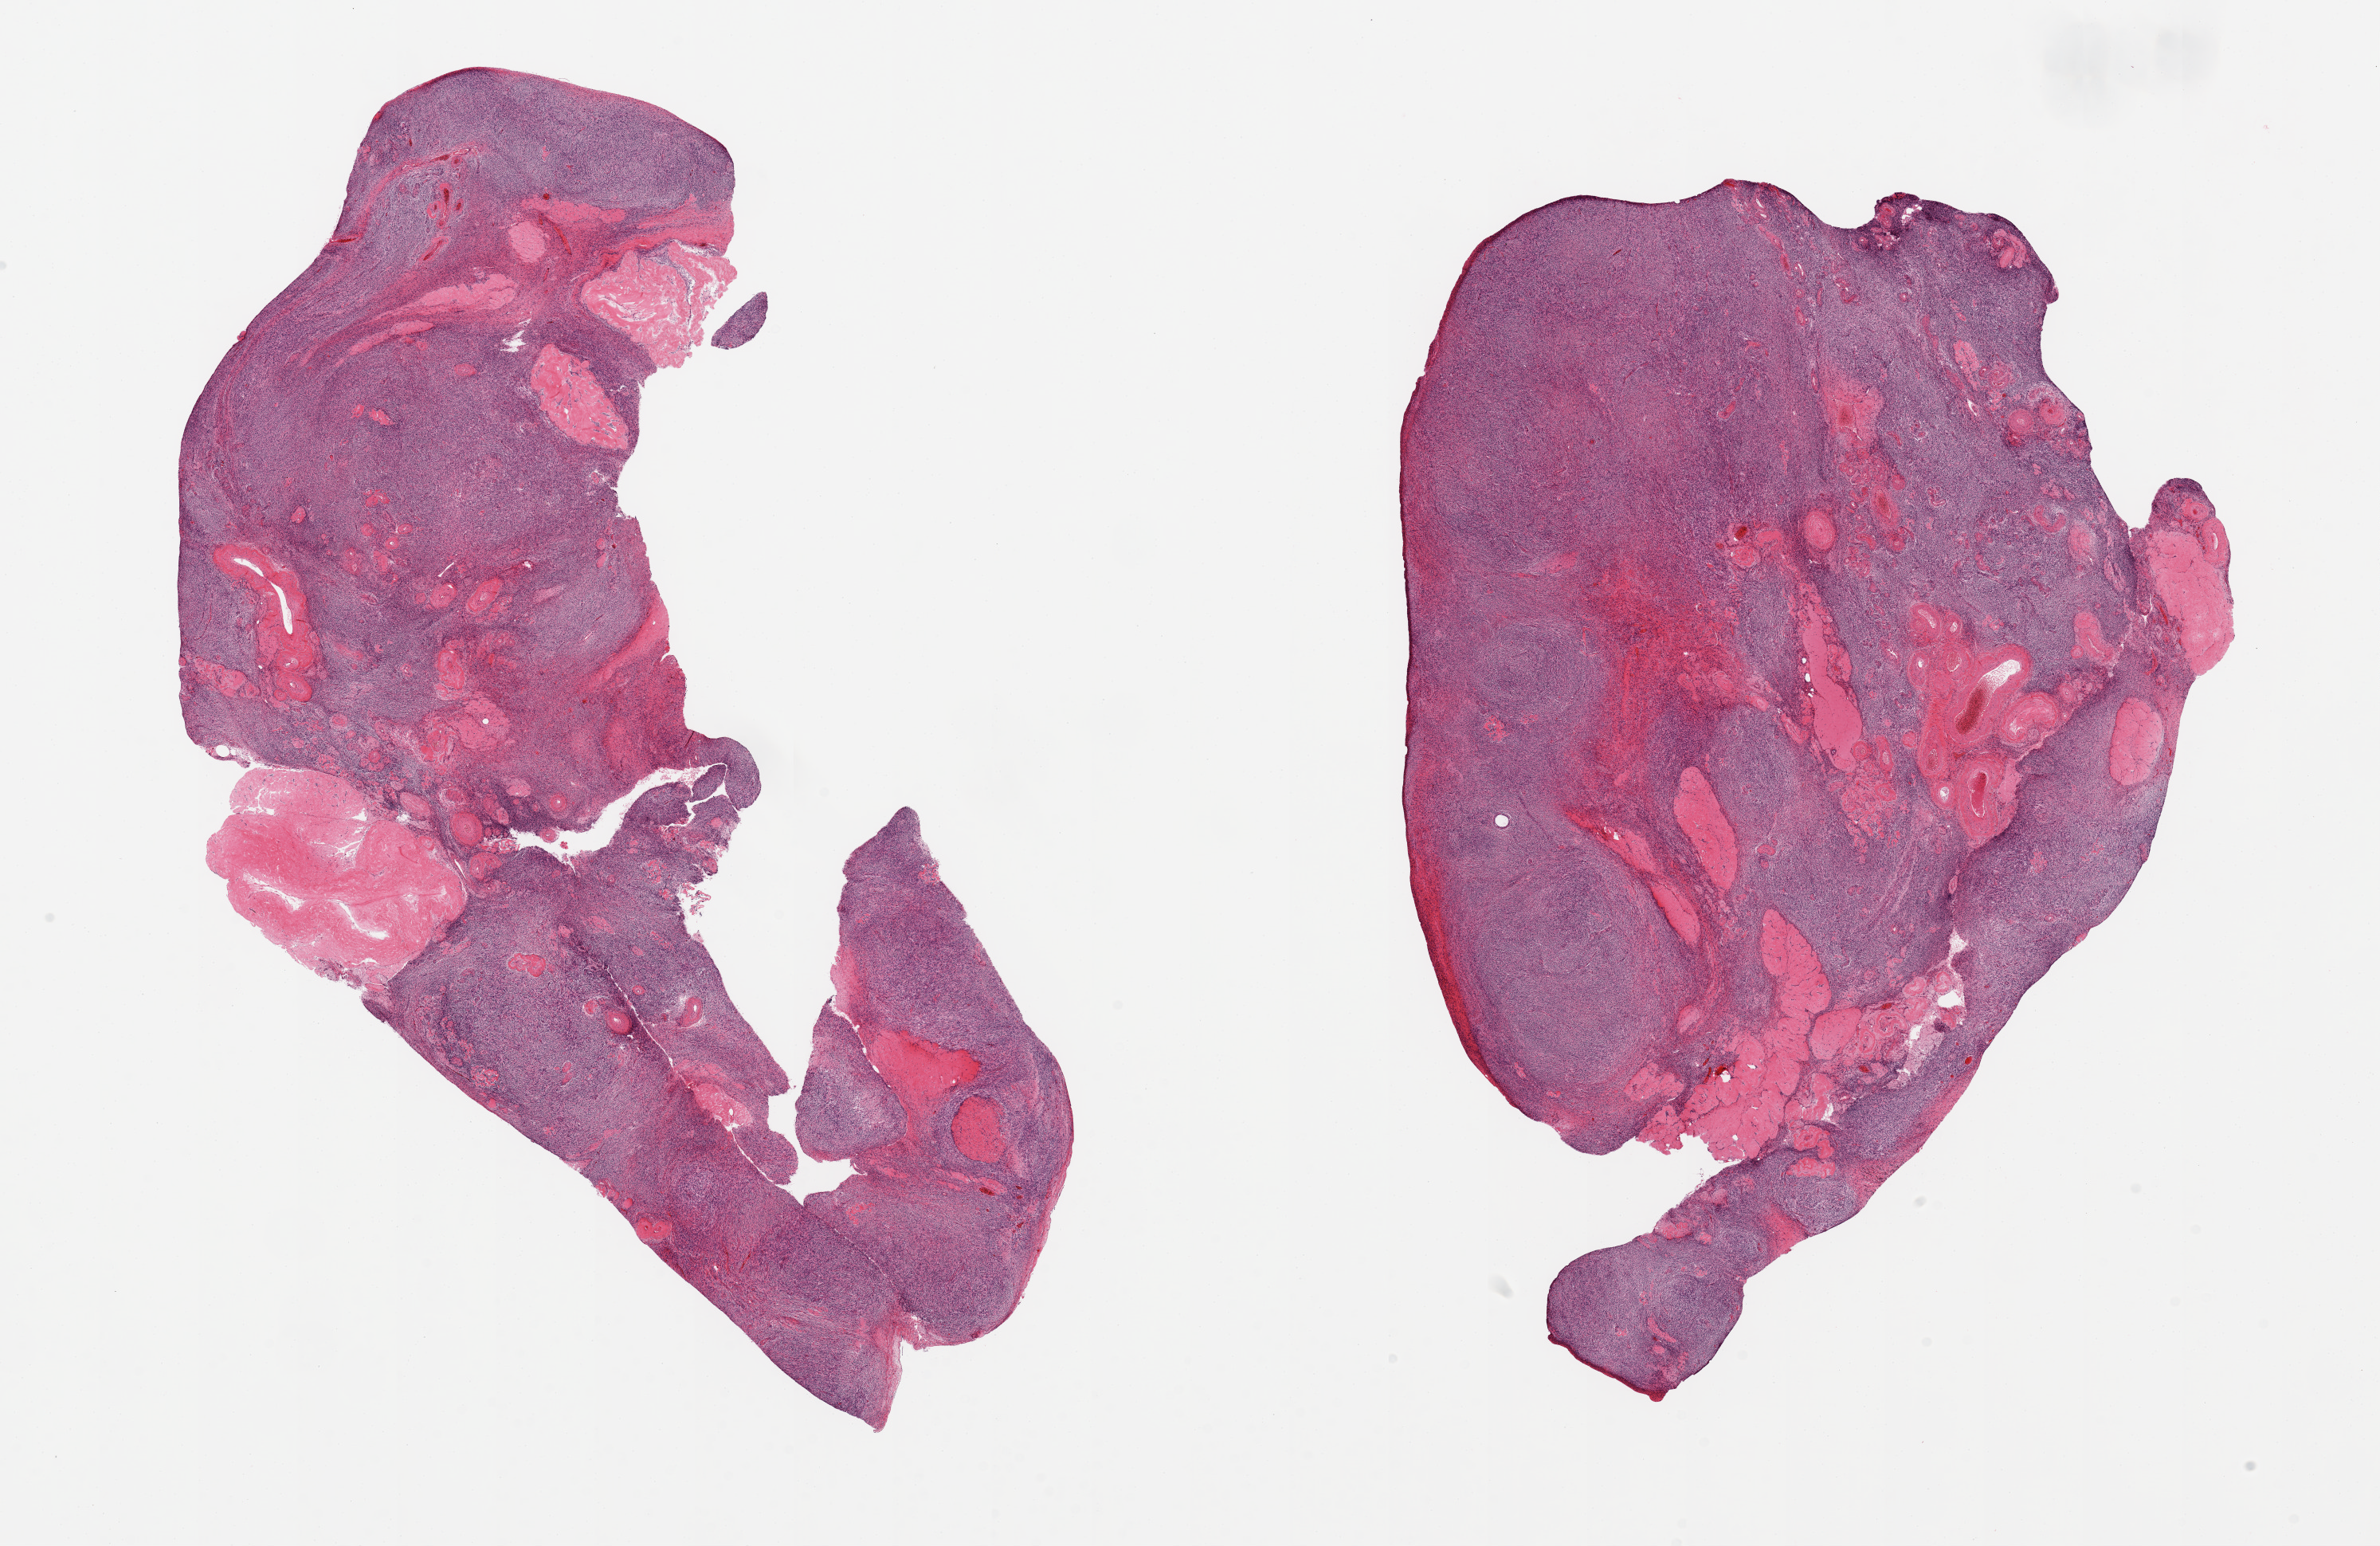
Whole-slide image, hematoxylin and eosin (H&E) stain, low-resolution overview of the scanned area, about 23.6 x 15.3 mm, PAXgene-fixed, paraffin-embedded tissue, section of ovary (target tissue), donor tissue sample. Donor sex: female.
Pathologist's review note for this sample: 2 pieces; ovarian cortex with corpora albicantia.